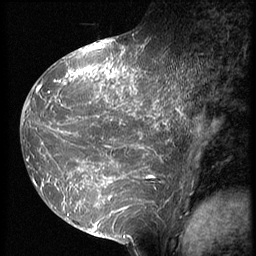
Breast MRI (dynamic contrast-enhanced), one sagittal slice; 3 images stored at this slice position (order not interpretable as contrast timing); 1.5 T; TE 4.2 ms, TR 9 ms; 256 × 256 image matrix, field of view 180 × 180 mm. Female patient, age 39 years. Case-level facts recorded for this patient, not image findings: setting: breast cancer imaged before/during neoadjuvant chemotherapy; receptor status: HER2-positive.
Annotated regions visible in this slice (semi-automatically segmented with operator editing):
- analysis volume of interest (the breast-tissue region the enhancement analysis was run in; not a lesion): box from (x=23, y=47) to (x=186, y=239) px
- tumour enhancement mask (voxels above the 140 % enhancement threshold inside the analysis volume of interest): (x=23, y=47)–(x=186, y=238)